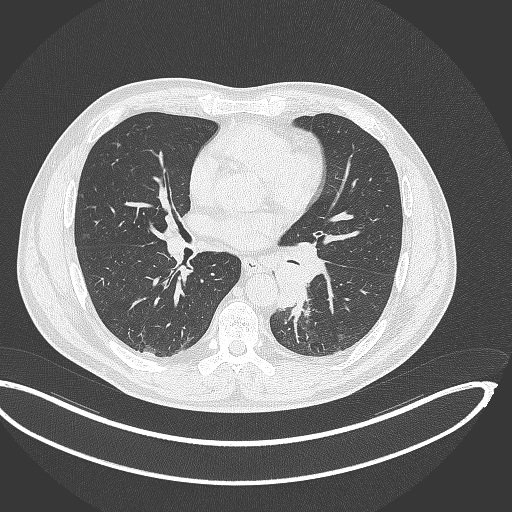
Chest CT, one axial slice. Position 176 of 362 along the scan axis. Reconstruction kernel B70f. 120 kVp. Lung window (W 1500 / L -600 HU). 512 × 512 image matrix, field of view 442 × 442 mm. Male patient, age 50 years. From the clinical record (not read from this slice): clinical TNM (as recorded): T2a N3 M0.
Structures marked on this image (rectangle marked by the reading radiologist):
- lung tumour (recorded histology: squamous cell carcinoma): box from (x=268, y=235) to (x=327, y=313) px